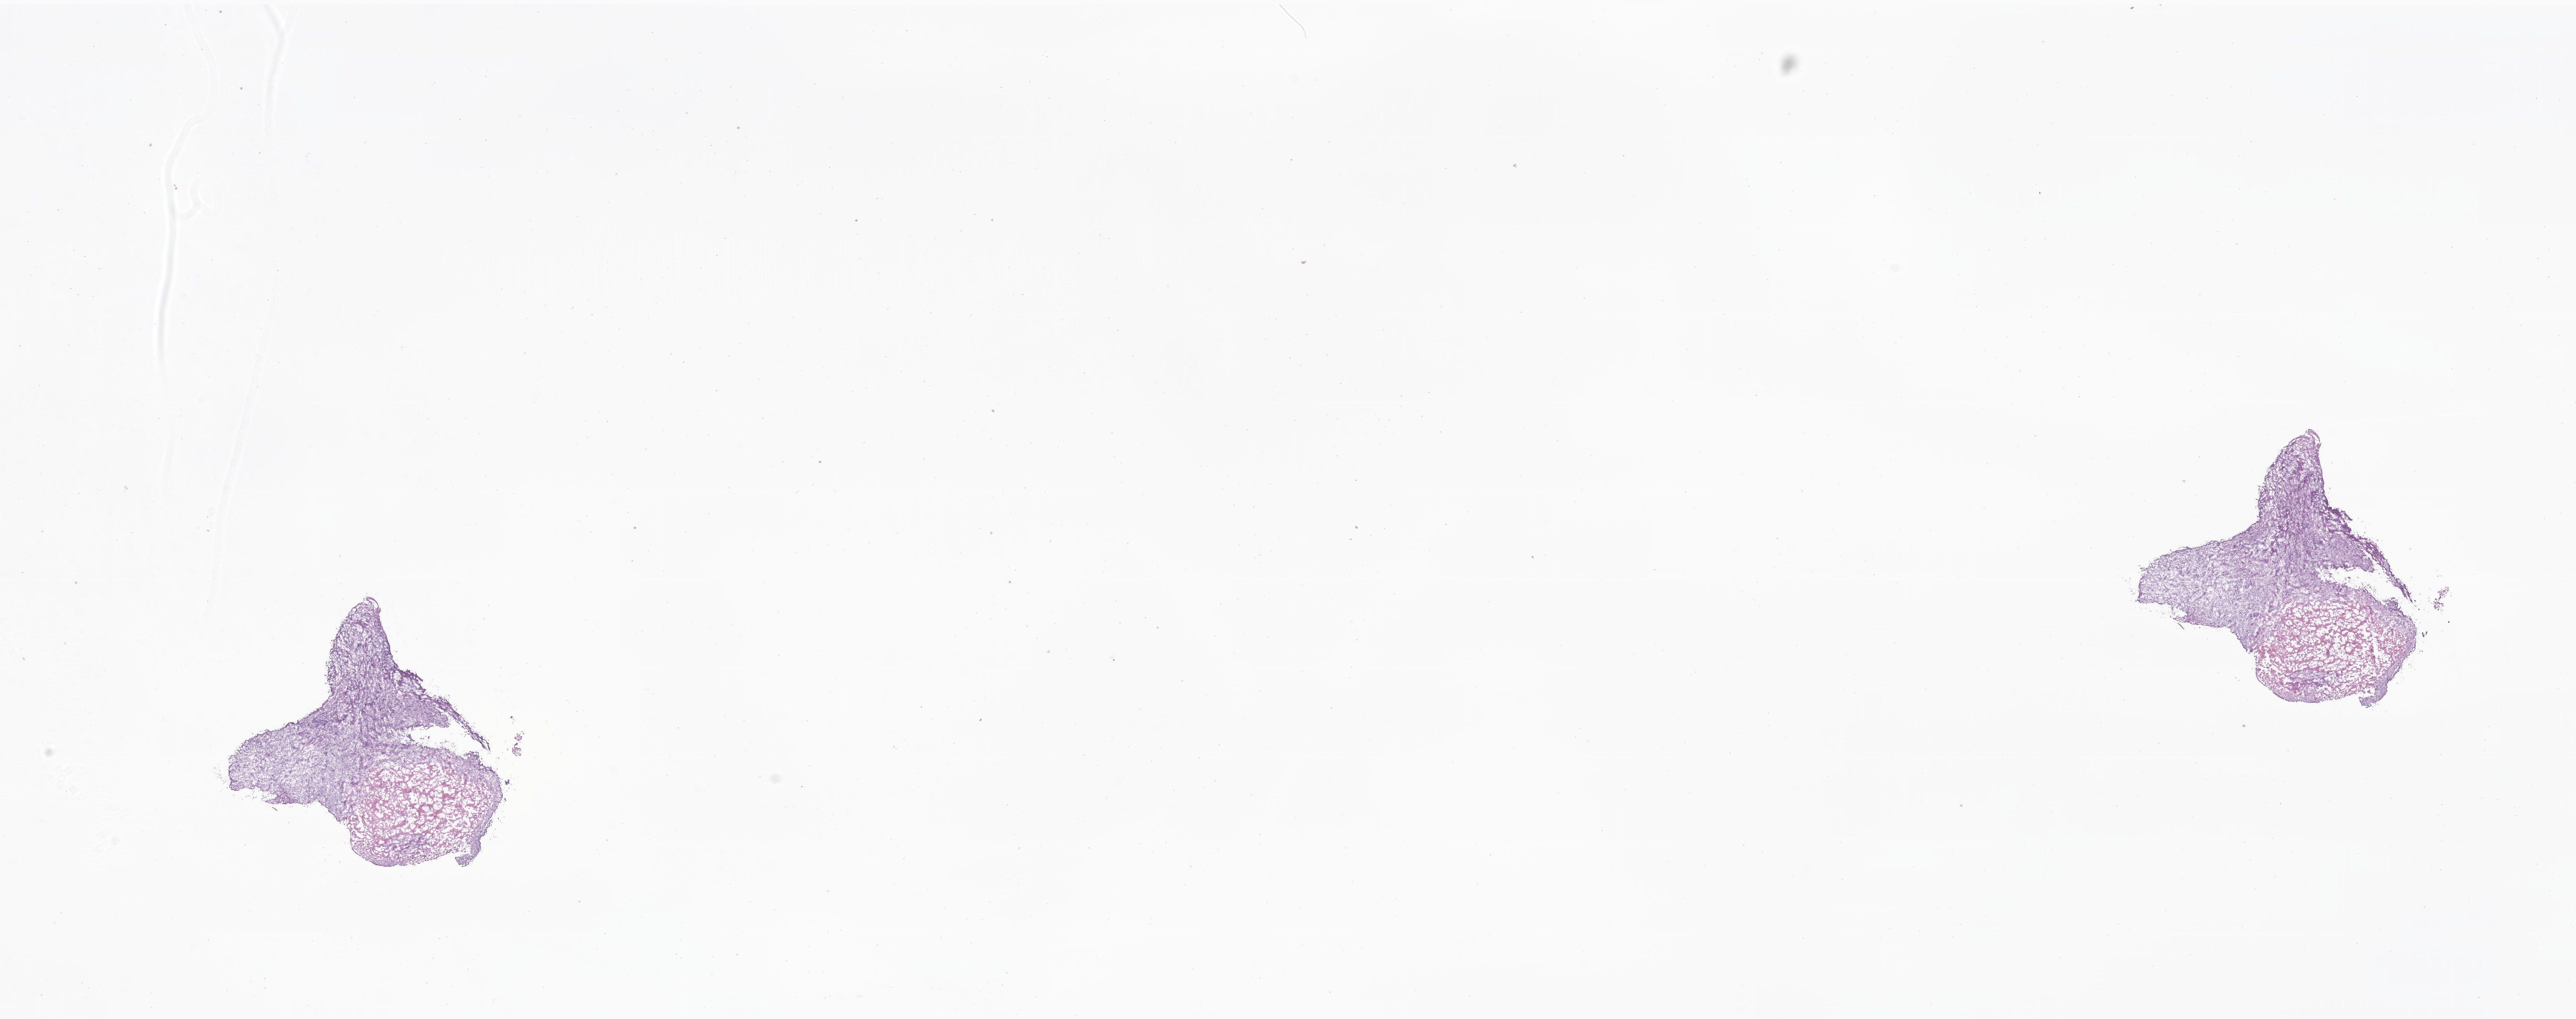
Haematoxylin and eosin whole-slide image of tumor tissue from the nasopharynx — shown as a low-resolution overview of the whole scanned area (about 31.1 x 12.3 mm), frozen section (OCT-embedded). Patient female; age 207 months.
Diagnosis: Carcinoma, NOS.